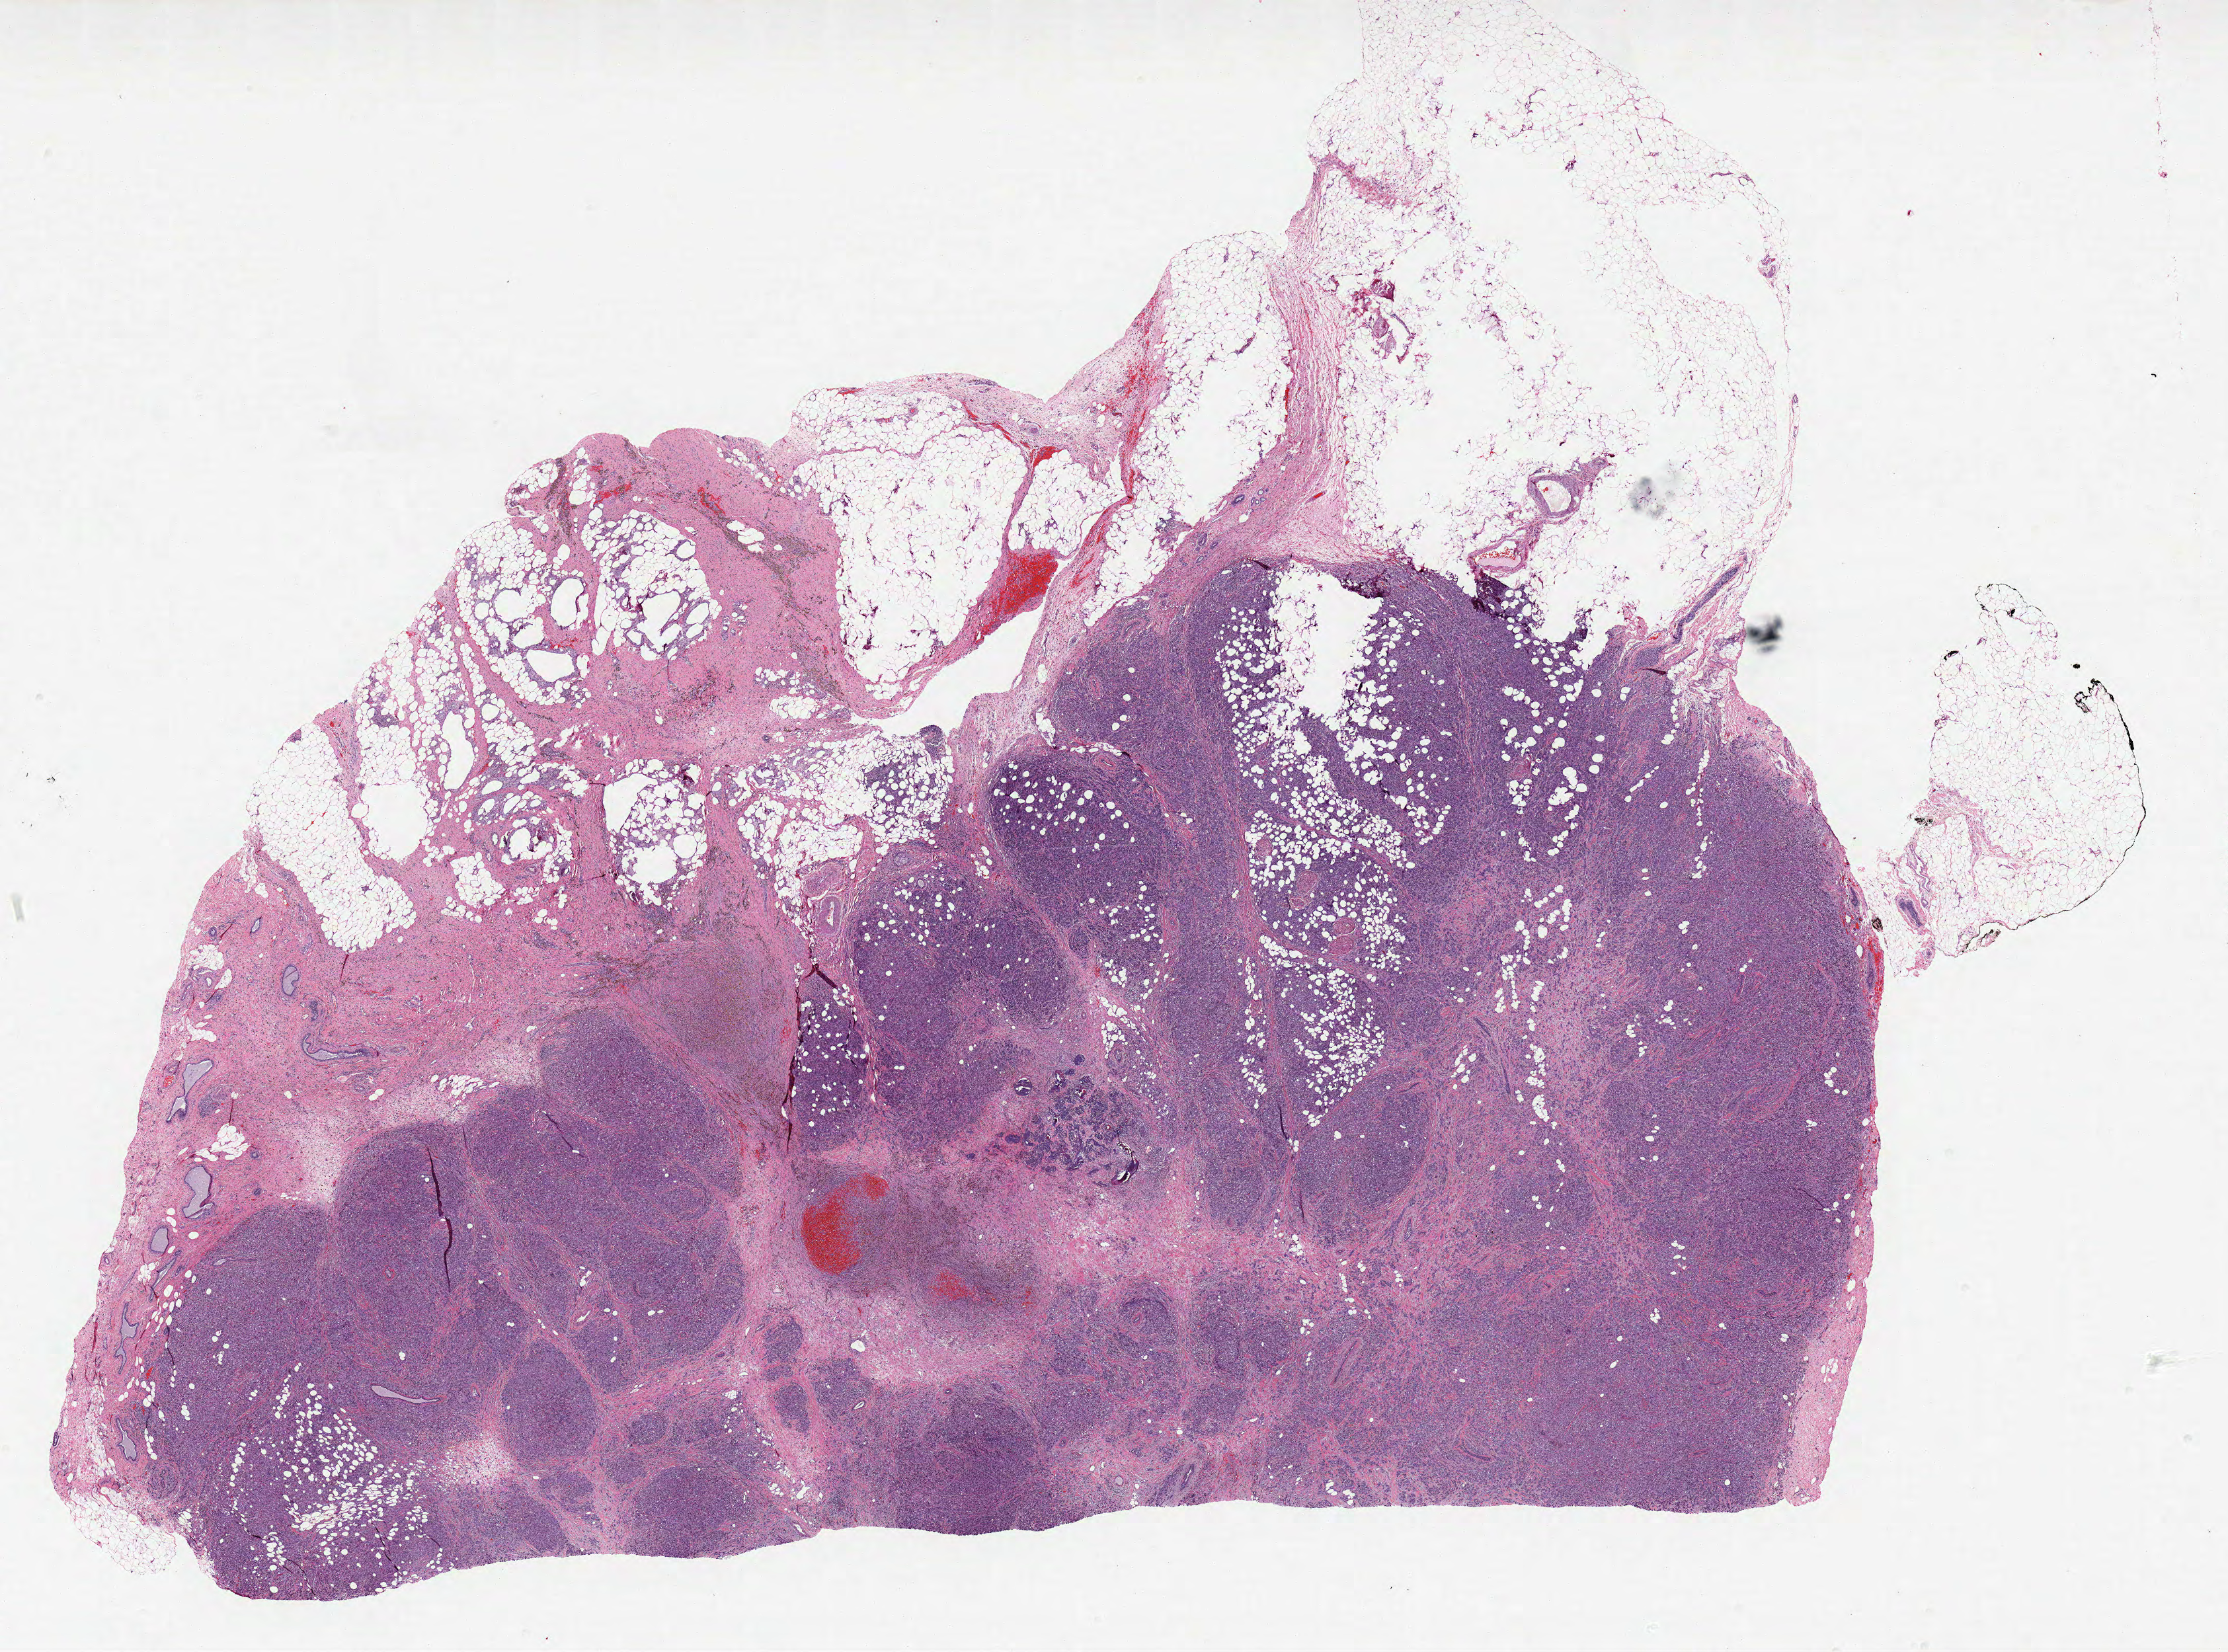
H&E whole-slide image — whole scanned area (about 26.9 x 19.9 mm, acquisition: 20x scan) shown as a low-resolution overview, formalin-fixed paraffin-embedded (FFPE) diagnostic section, breast, primary tumour sample. Patient: female, age at initial diagnosis 69 years.
* TNM: T2 N0 (i-) M0
* histologic diagnosis: Lobular carcinoma, NOS
* lymph nodes positive (case pathology): 0 of 5 examined
* AJCC pathologic stage: IIA (7th edition)